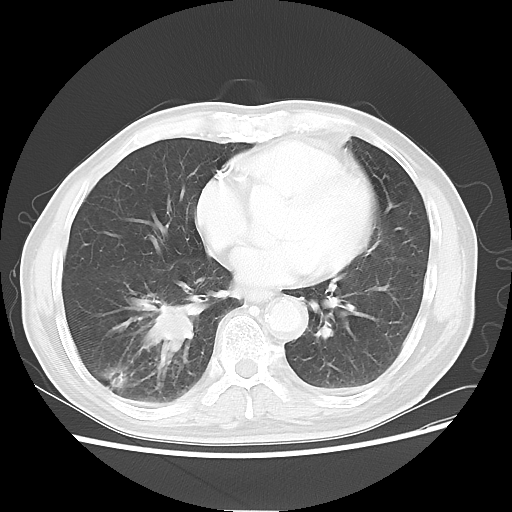
Chest CT, one axial slice. Slice 23 of 58 in the series (ordered by position). 120 kVp. Lung window (W 1500 / L -600 HU). 5 mm slice thickness. 512 × 512 image matrix, field of view 360 × 360 mm. Patient: male, 74 years. From the clinical record (not read from this slice): clinical TNM (as recorded): T1c N1 M1.
Annotated regions visible in this slice (rectangle marked by the reading radiologist):
- lung tumour (recorded histology: adenocarcinoma): bounding box <130,286,197,371> (left, top, right, bottom; pixels)